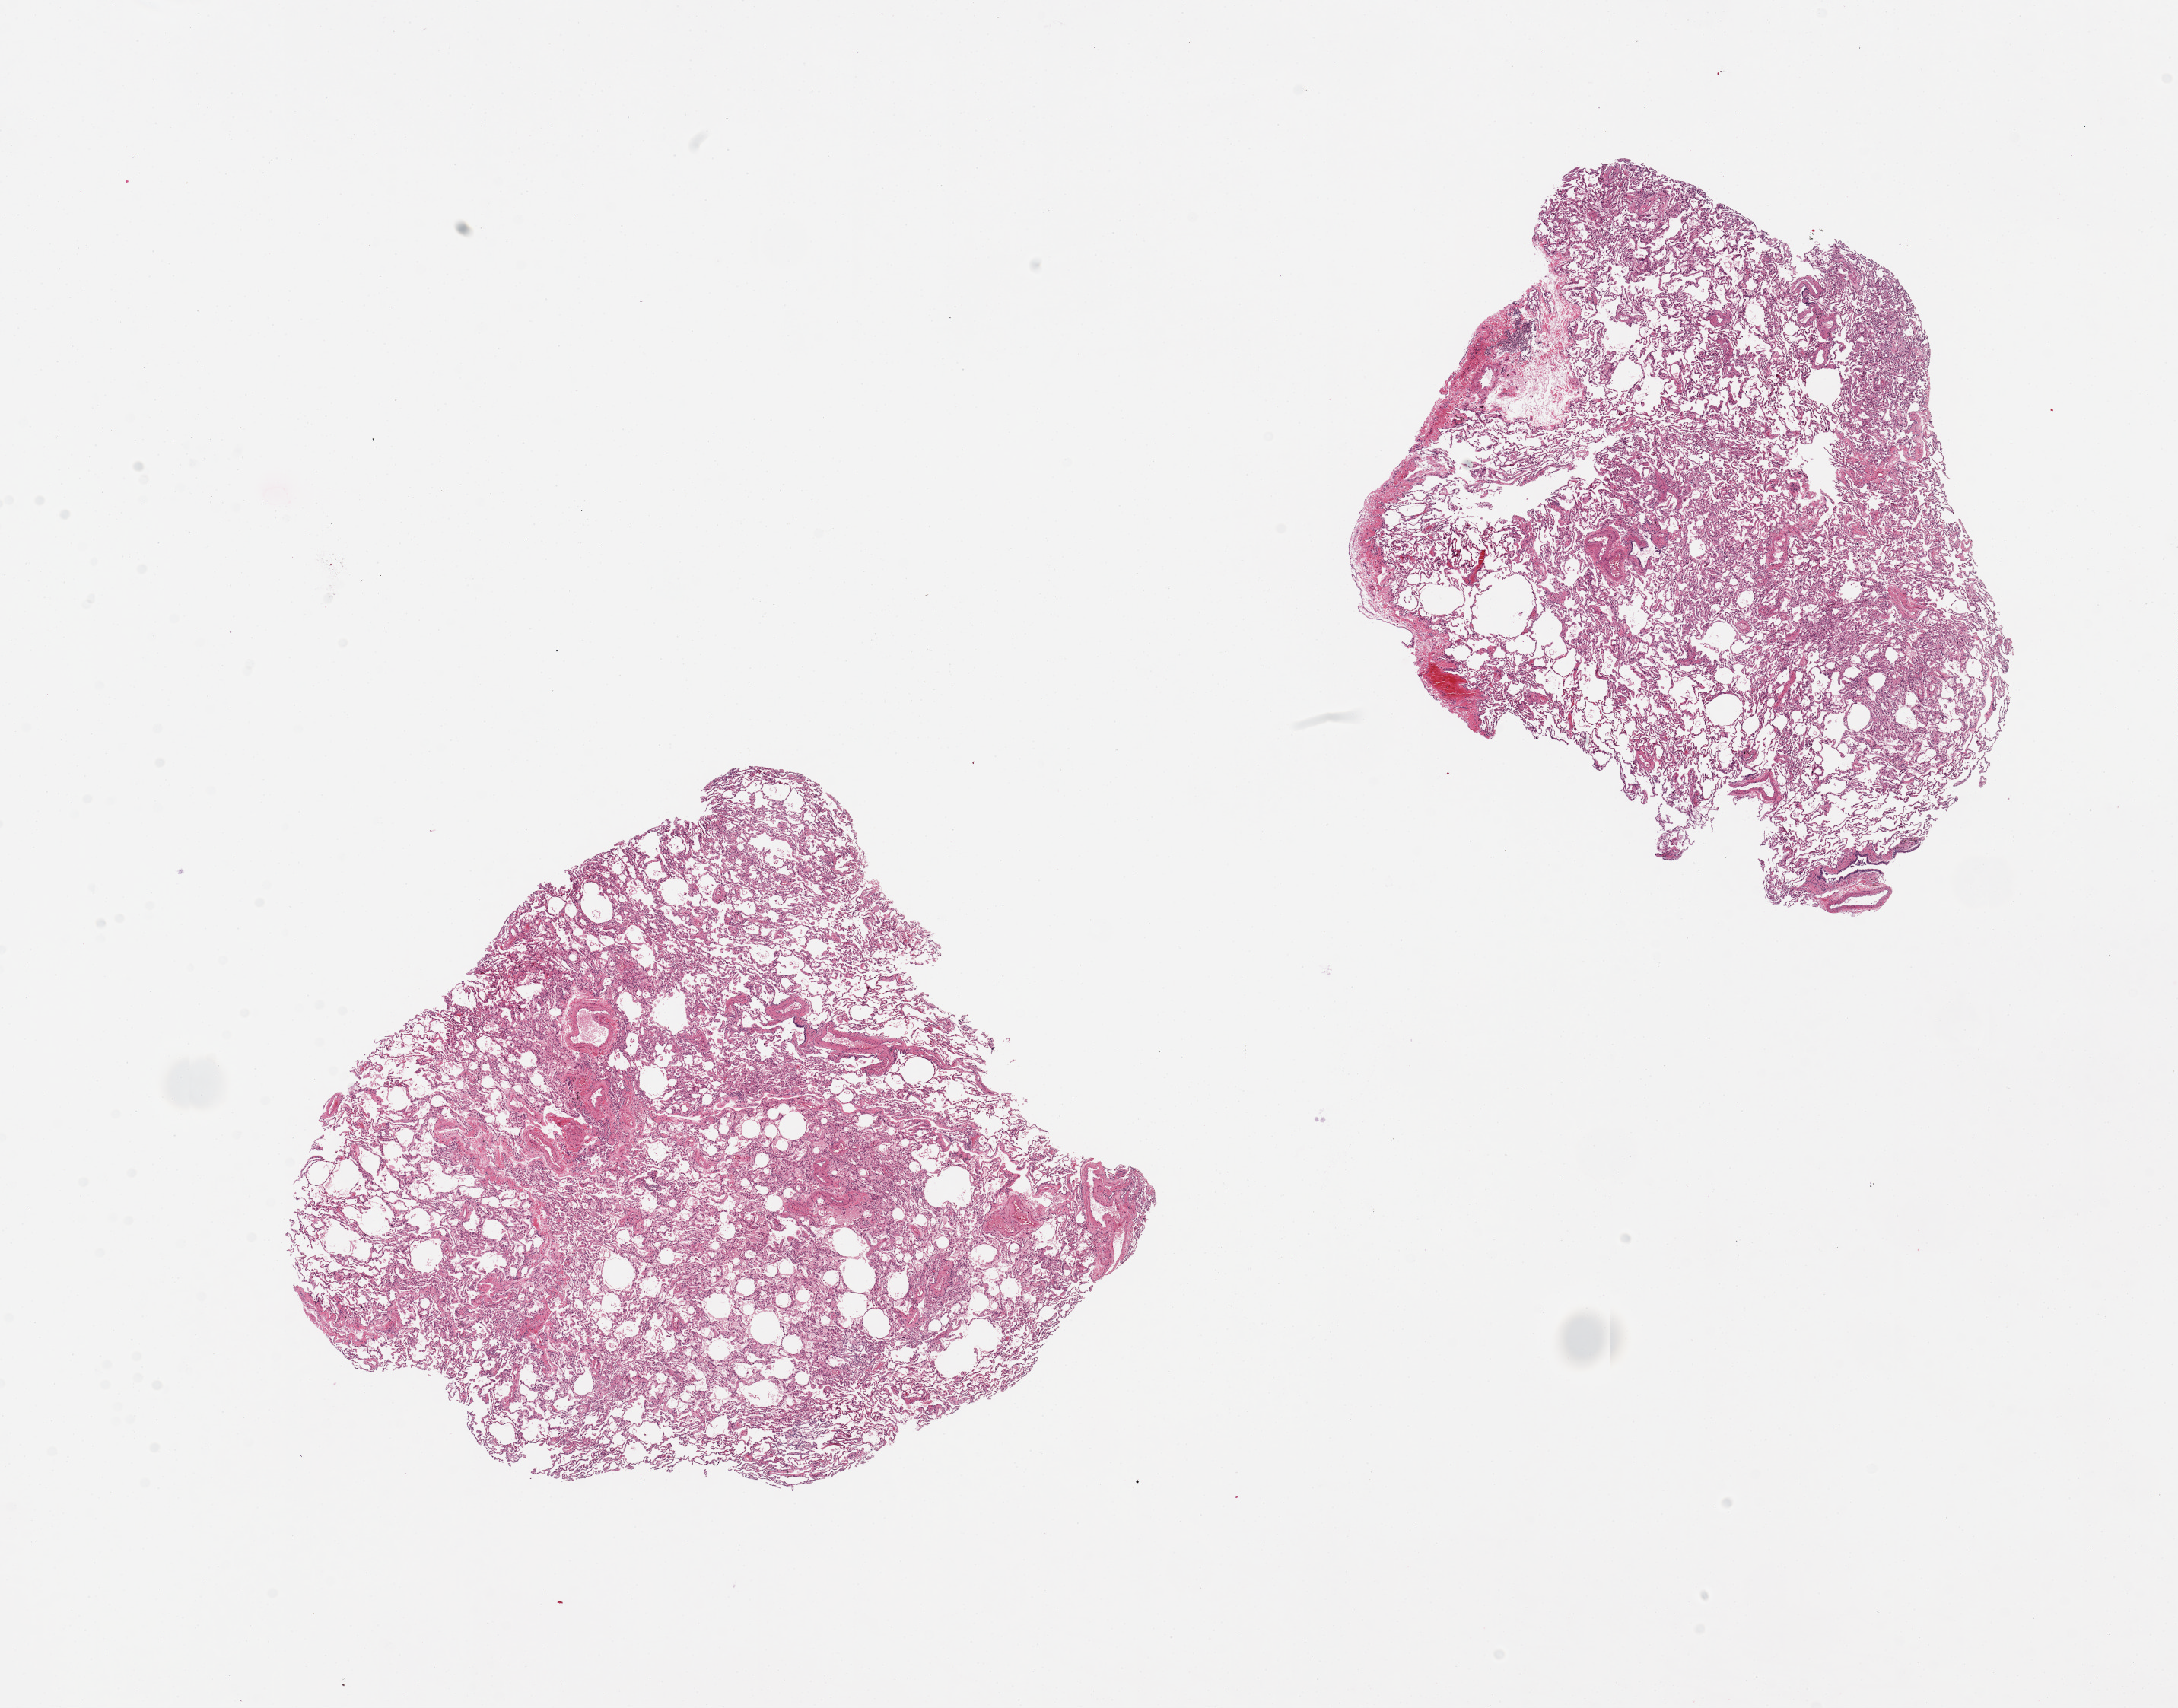
Whole-slide image, haematoxylin and eosin stain — low-resolution overview of the scanned area, about 22.6 x 17.8 mm (slide scanned at 20x). PAXgene-fixed paraffin-embedded (PFPE) section. Section of lung (target tissue). Tissue donor sample. Male donor.
- reviewer comment on this tissue sample: 2 pieces, 8x7 & 8x6.5mm; focal emphysema